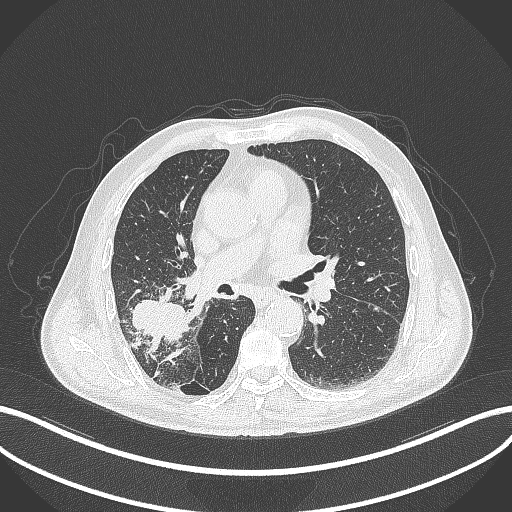
Chest CT, one axial slice; position 229 of 429 along the scan axis; 120 kVp; lung window (W 1500 / L -600 HU); 512 × 512 image matrix, field of view 400 × 400 mm. Patient: male, 72 years. From the clinical record (not read from this slice): clinical TNM (as recorded): T3 N2 M0.
Structures marked on this image (rectangle marked by the reading radiologist):
- lung tumour (recorded histology: adenocarcinoma): box from (x=125, y=293) to (x=195, y=346) px